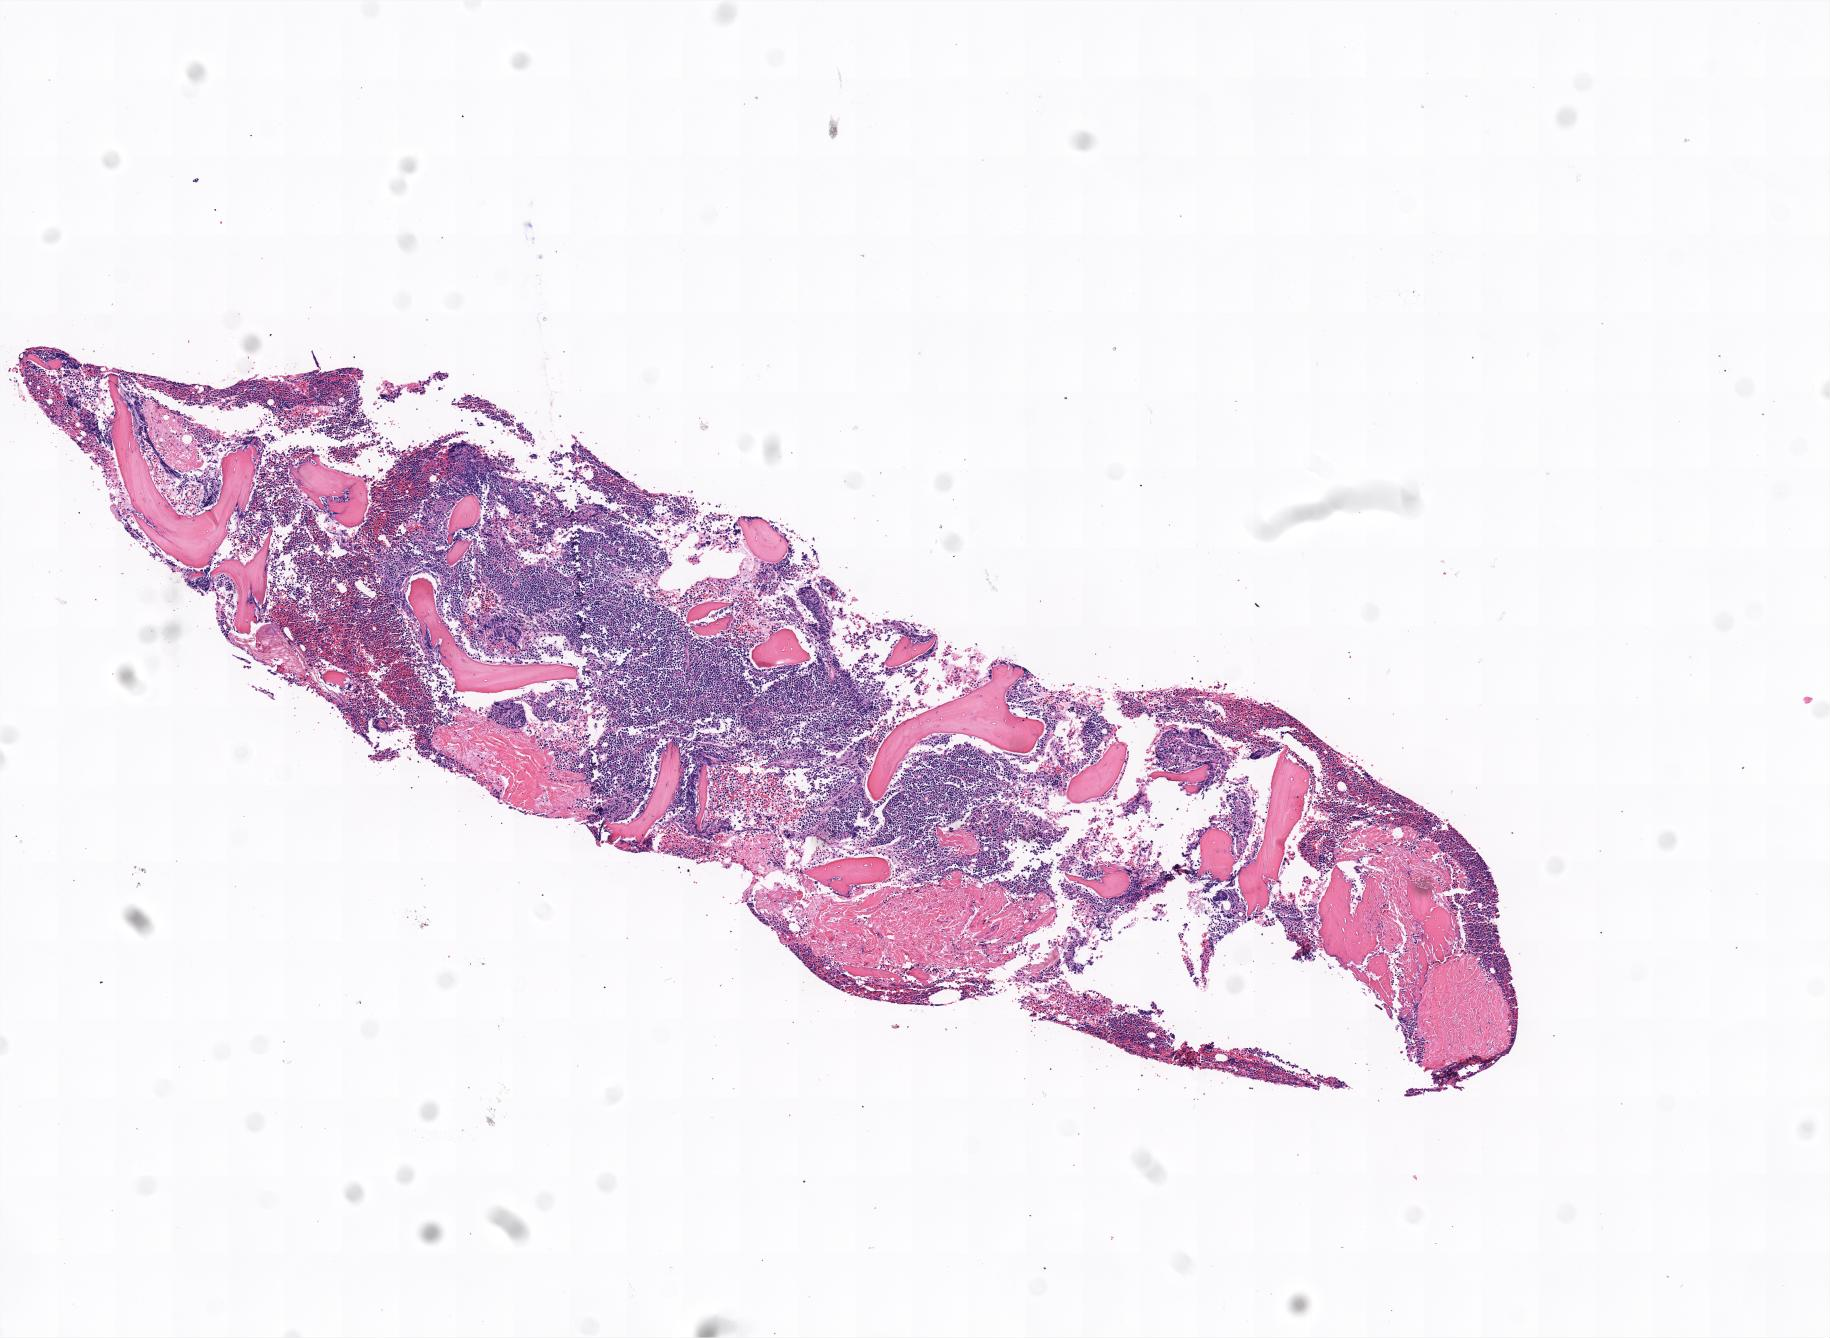
Hematoxylin and eosin (H&E) whole-slide image, low-resolution overview of the scanned area; tumor tissue; anatomic site: bone marrow. Female patient; age at initial diagnosis 3 years.
Histologic diagnosis: Burkitt lymphoma, NOS.